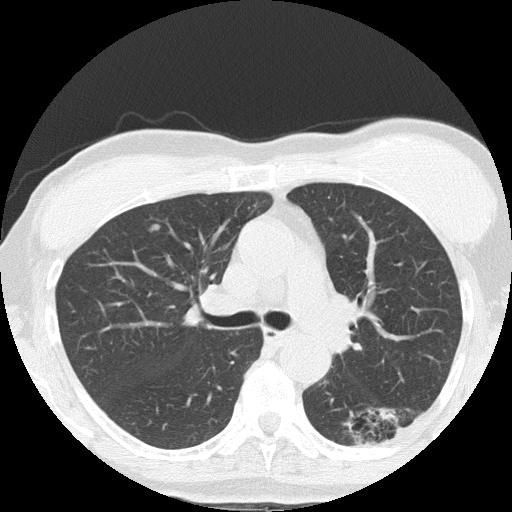
Low-dose screening chest CT, axial slice; third annual screen; lung window (W 1500 / L -600 HU); 120 kVp; slice 58 of 152 in the series. Female, age 64 years at enrolment. Former smoker at enrolment.
Expert reader's lesion annotation, bounding box [x1, y1, x2, y2] px = [347, 385, 434, 454]. The screening reader recorded 3 non-calcified nodules or masses ≥4 mm on this exam (right upper lobe, left lower lobe, right middle lobe); which of them this box marks is not recorded. Lung cancer was diagnosed 212 days after this screen: adenocarcinoma, NOS, left lower lobe, moderately differentiated (G2), stage IA (AJCC 6th edition), 17 mm at pathology.